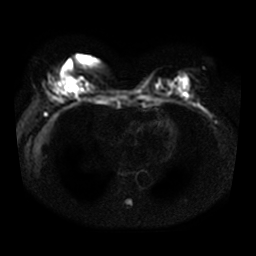
Breast MRI, one axial slice; slice 16 of 36 in the series (ordered by position); diffusion-weighted series; image 2 of 4 stored at this slice position (different b-values; order by instance number); 3 T; 5 mm slice thickness; 256 × 256 image matrix. Female patient.
Annotated regions visible in this slice (outlined manually by an expert reader):
- tumour on diffusion-weighted imaging: bounding box (x1, y1, x2, y2) in pixels: (68, 82, 78, 93)